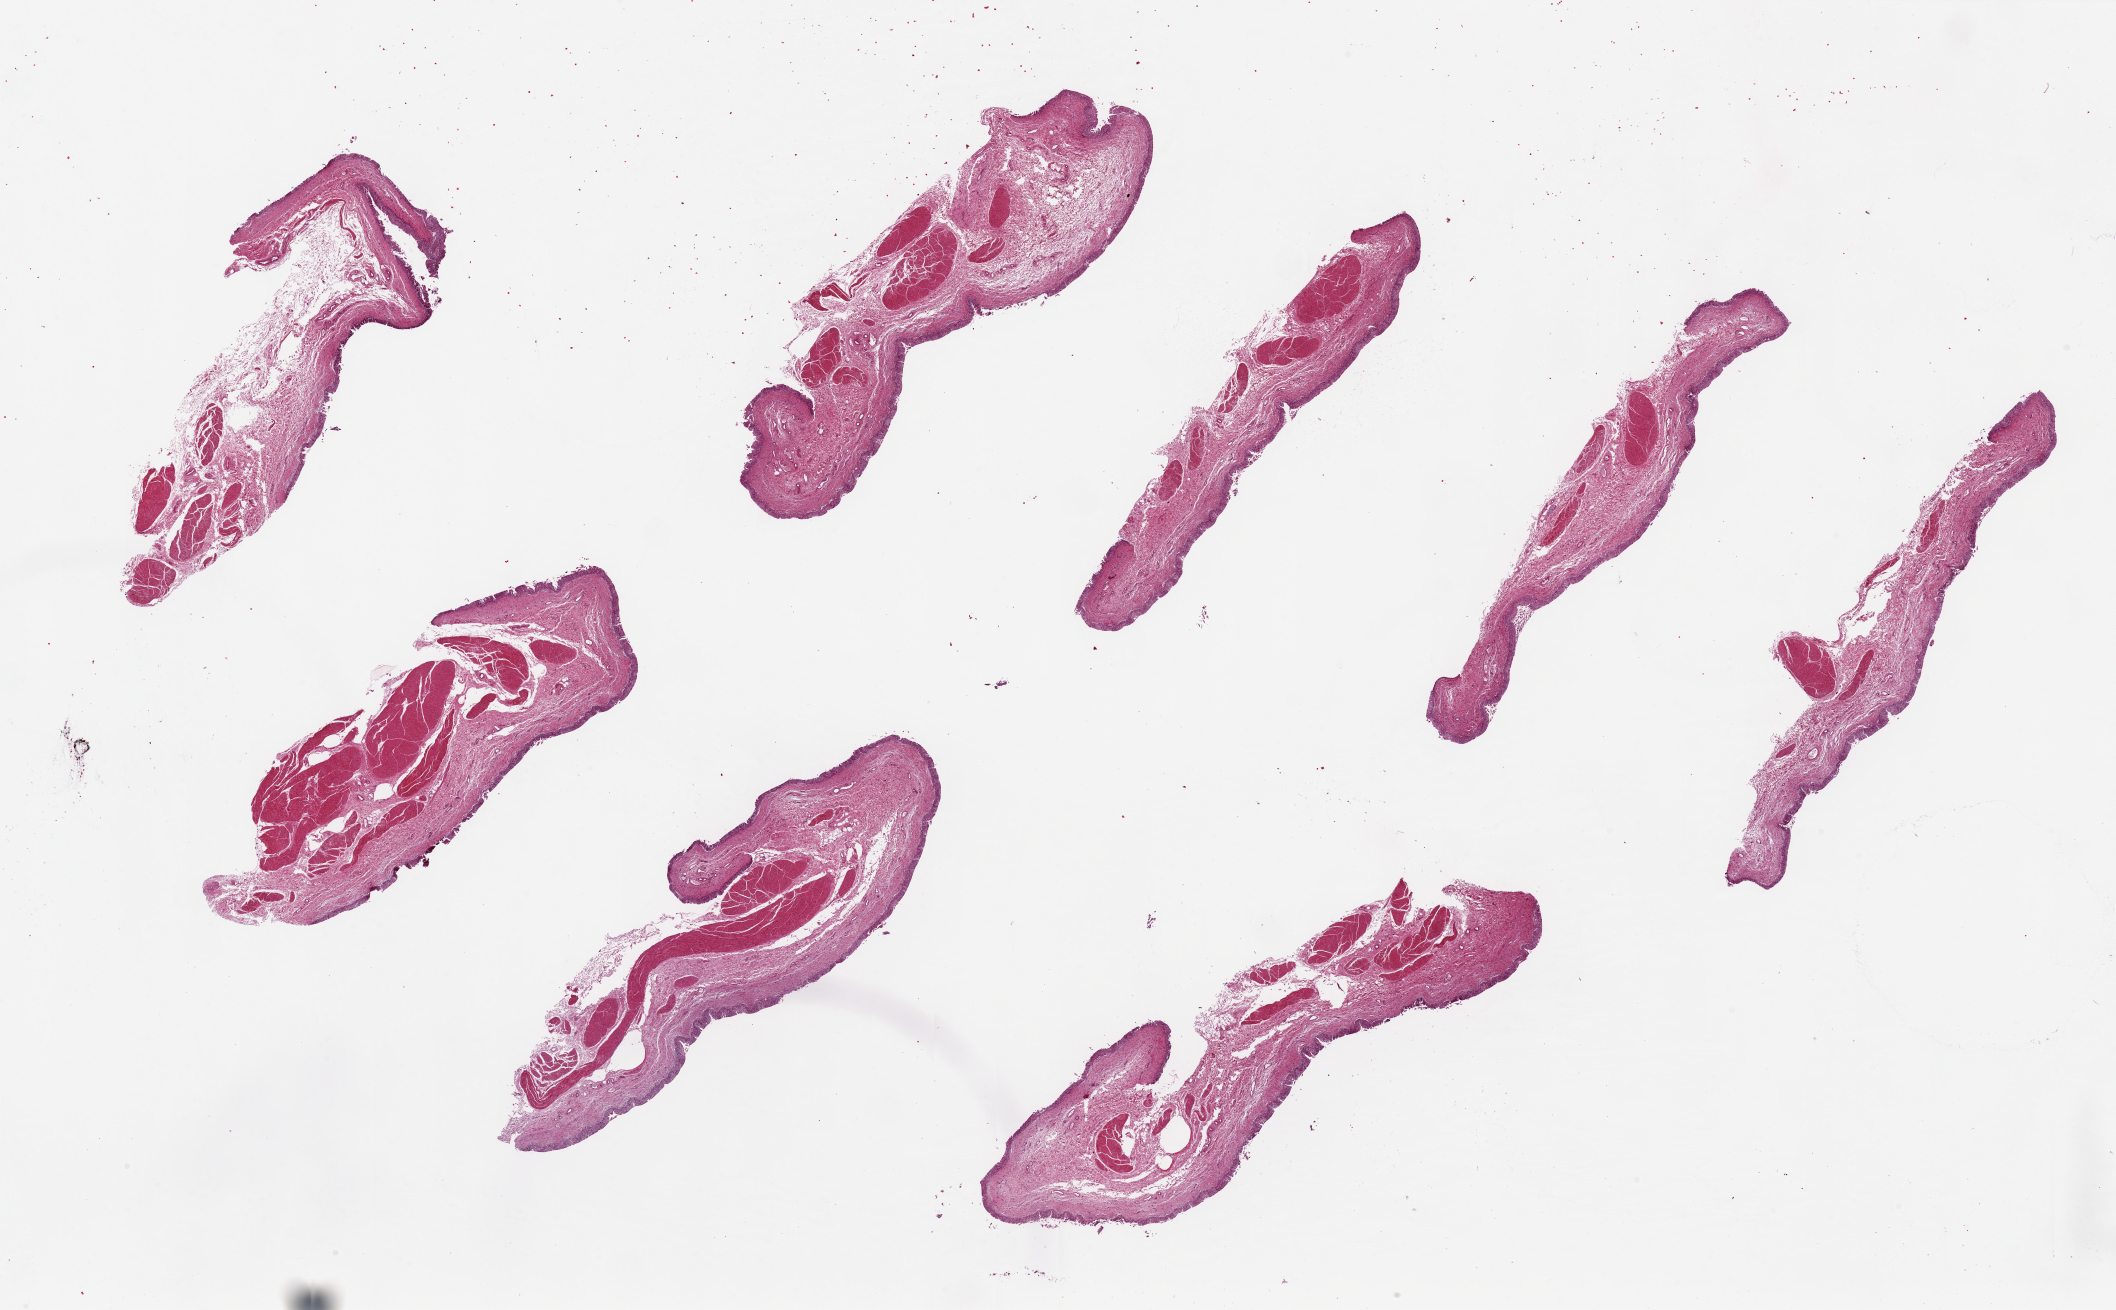
H&E whole-slide image — a low-resolution overview of the entire scanned area, about 33.5 x 20.7 mm. PAXgene-fixed paraffin-embedded (PFPE) section. Target tissue: urinary bladder. Tissue donor sample. Male donor.
- pathologist's review note for this sample: 8 pieces, up to 10x3 mm; preserved mucosa on all